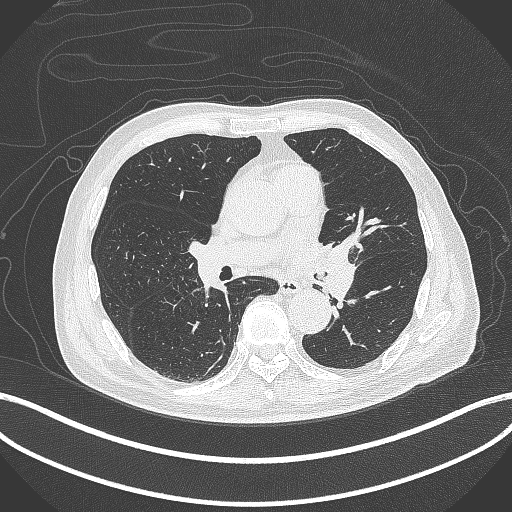
Chest CT, one axial slice. Position 228 of 417 along the scan axis. Reconstruction kernel B70f. 120 kVp. Lung window (W 1500 / L -600 HU). 1 mm slice thickness. 512 × 512 image matrix, field of view 400 × 400 mm. Male patient, age 77 years. From the clinical record (not read from this slice): clinical TNM (as recorded): T3 N1 M0.
Outlined on this slice (rectangle marked by the reading radiologist):
- lung tumour (recorded histology: adenocarcinoma): bounding box [x1, y1, x2, y2] px = [316, 237, 358, 302]